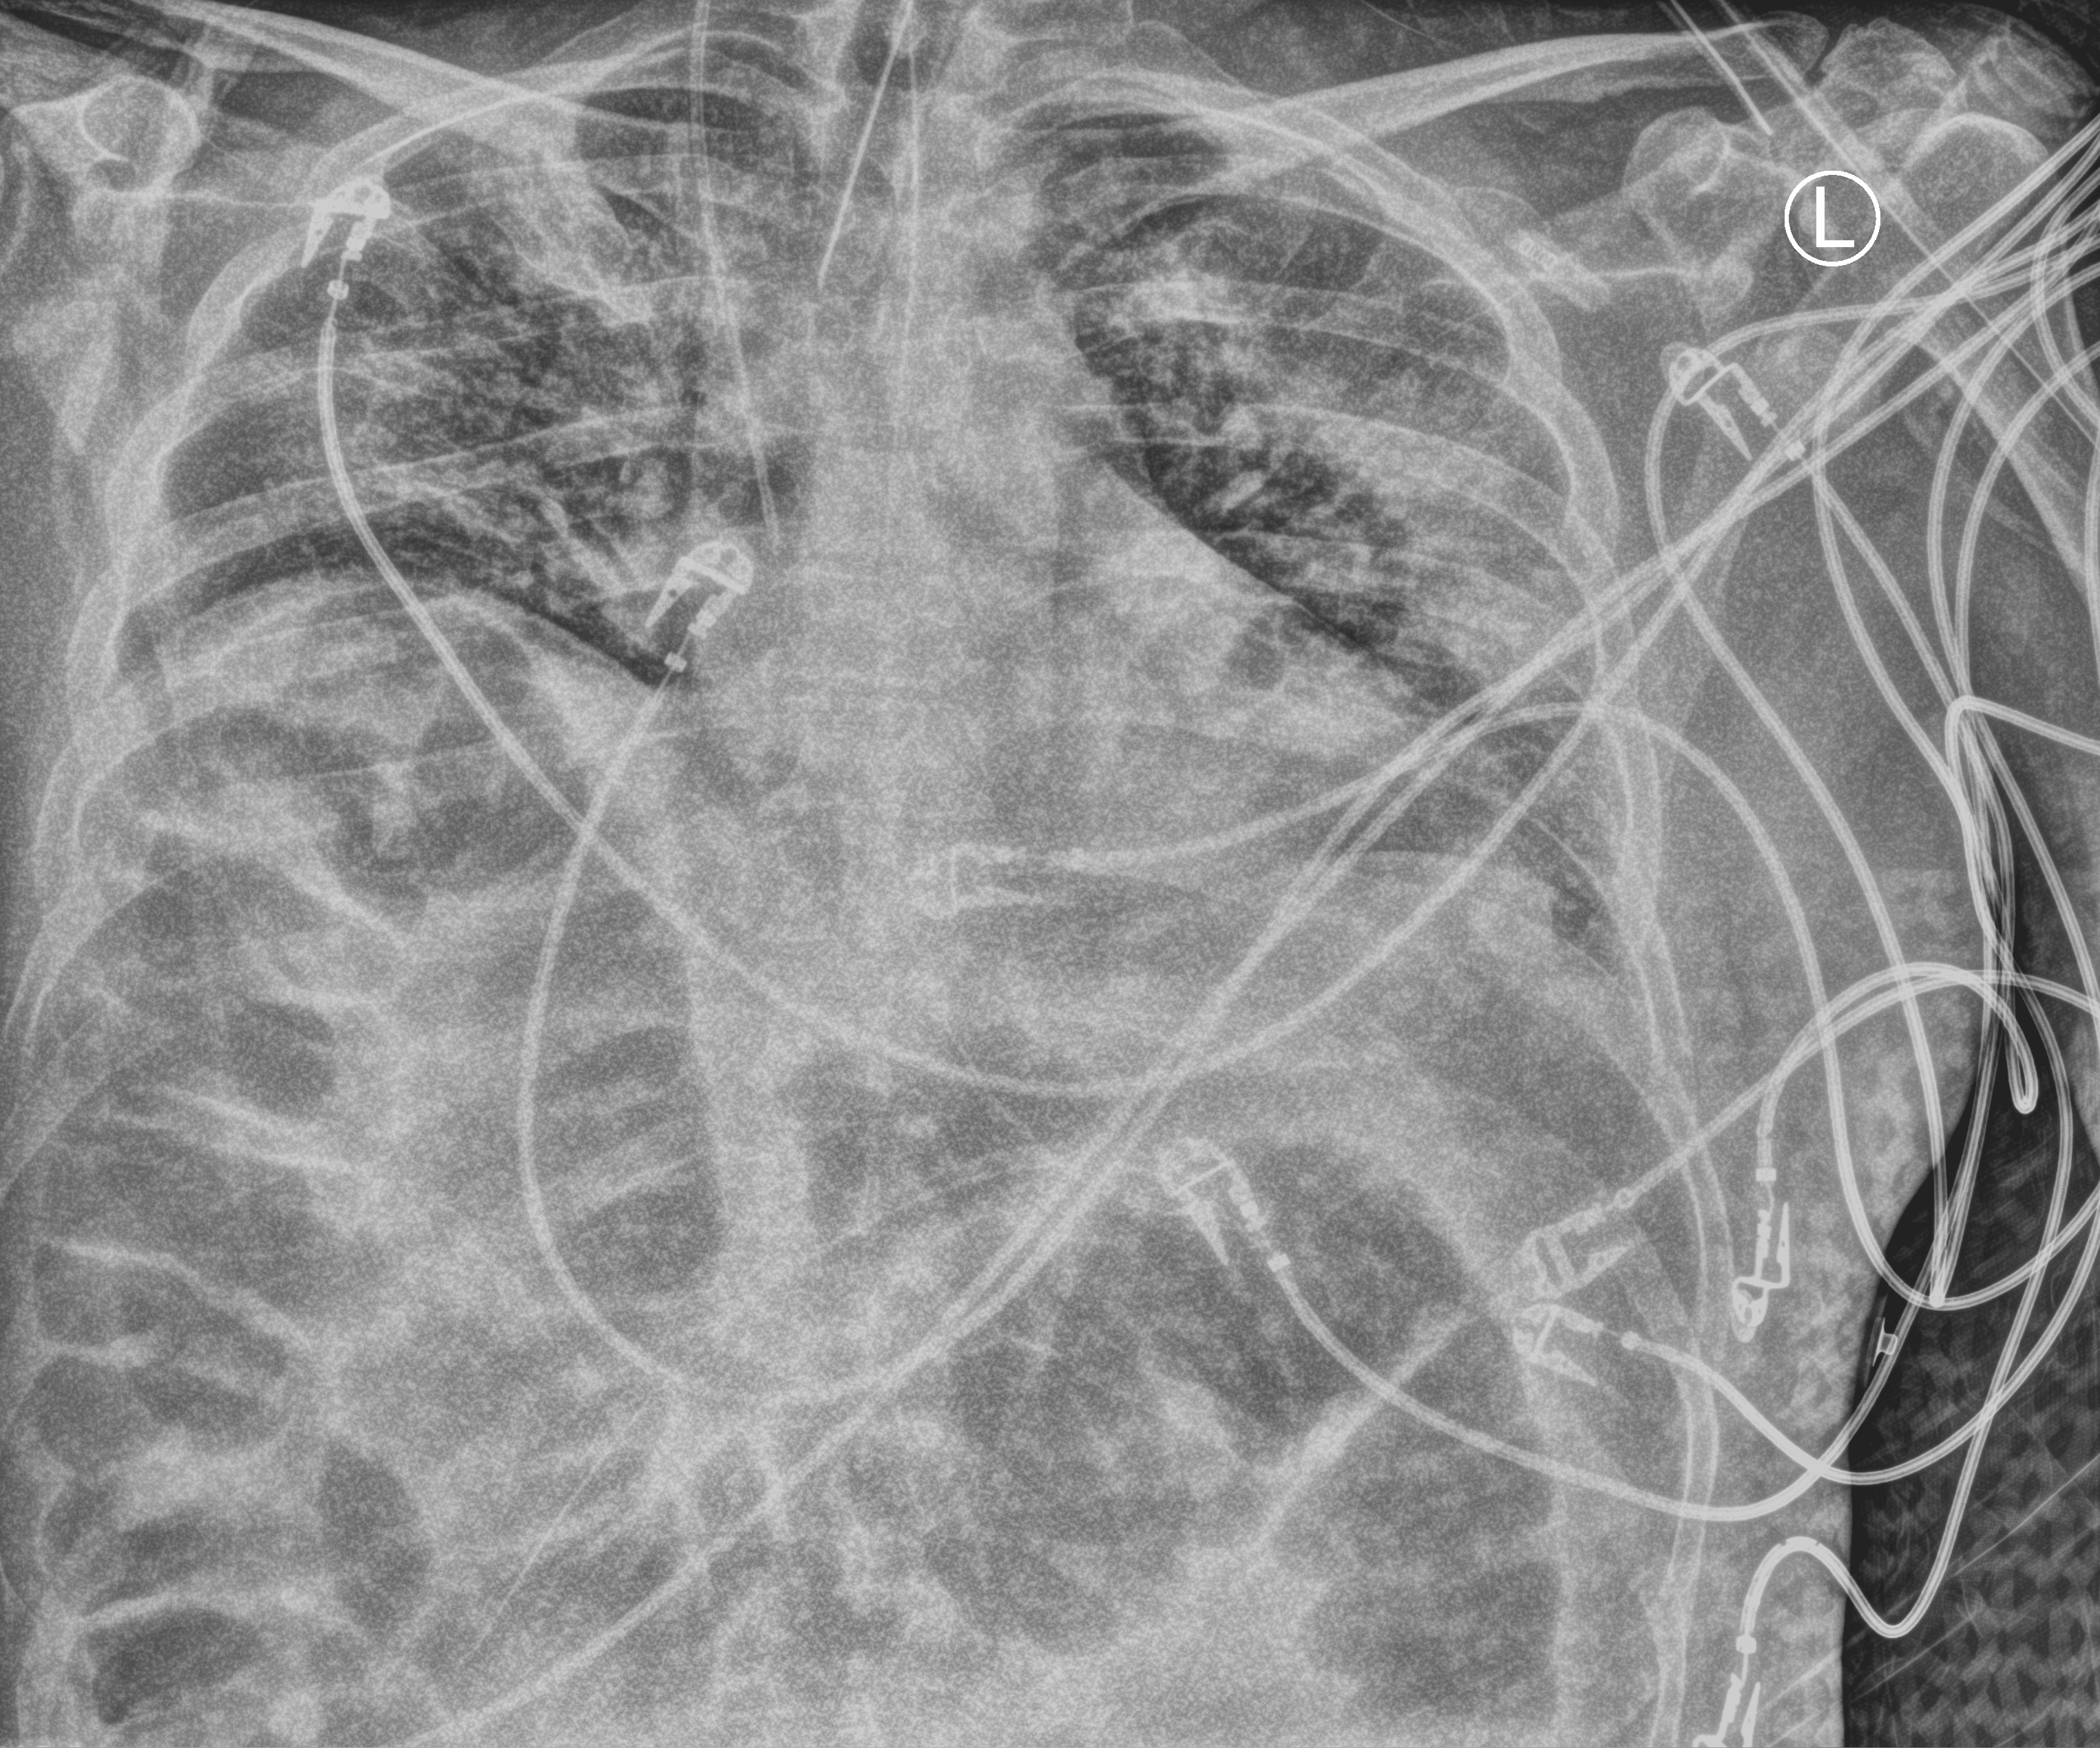
Bedside chest radiograph (computed radiography), anteroposterior (AP) projection. Patient hospitalised with COVID-19; male, aged 18–59 years.
Admission-level facts for this patient (not findings on this image; timing relative to this image not recorded):
- admitted to intensive care during this hospital stay: yes
- chronic kidney disease (admission record): no